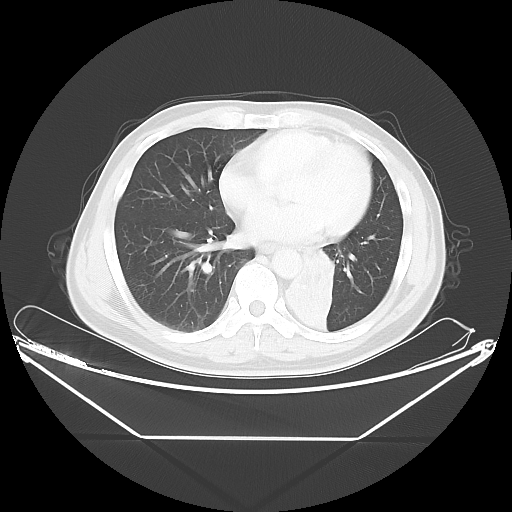
Chest CT, one axial slice; lung window (W 1500 / L -600 HU); 512 × 512 image matrix, field of view 438 × 438 mm. Patient: male, 58 years. Case-level facts recorded for this patient, not image findings: clinical TNM (as recorded): T3 N3 M0.
Outlined on this slice (bounding box drawn by a radiologist):
- lung tumour (recorded histology: squamous cell carcinoma): bounding box [x1, y1, x2, y2] px = [284, 240, 362, 345]